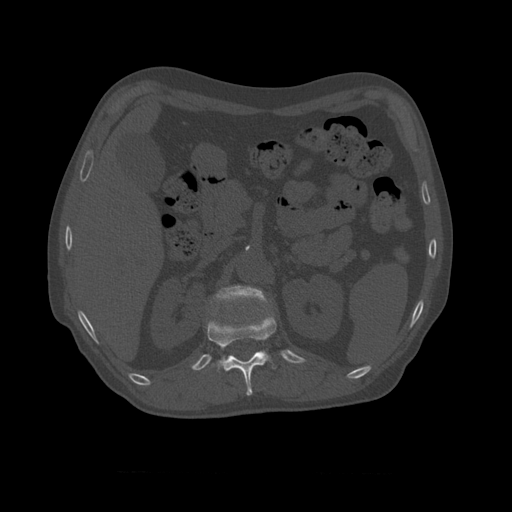
CT including the spine, one axial slice; position 374 of 450 along the scan axis; reconstruction kernel STANDARD; 120 kVp; bone window (W 1800 / L 400 HU); 512 × 512 image matrix, field of view 405 × 405 mm. Patient age 75 years. Case-level facts recorded for this patient, not image findings: primary cancer: prostate.
Annotated regions visible in this slice (semi-automatically segmented with operator editing):
- L1 vertebra: bounding box (x1, y1, x2, y2) in pixels: (210, 285, 270, 305)
- T11 vertebra: (207, 313, 277, 396)